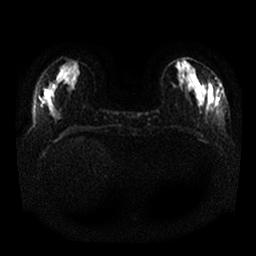
Breast MRI, one axial slice. Position 9 of 25 along the scan axis. Diffusion-weighted series; image 2 of 4 stored at this slice position (different b-values; order by instance number). 1.5 T. 4 mm slice thickness. 256 × 256 image matrix. Female patient.
Structures marked on this image (outlined manually by an expert reader):
- tumour on diffusion-weighted imaging: bounding box [x1, y1, x2, y2] px = [212, 89, 220, 107]